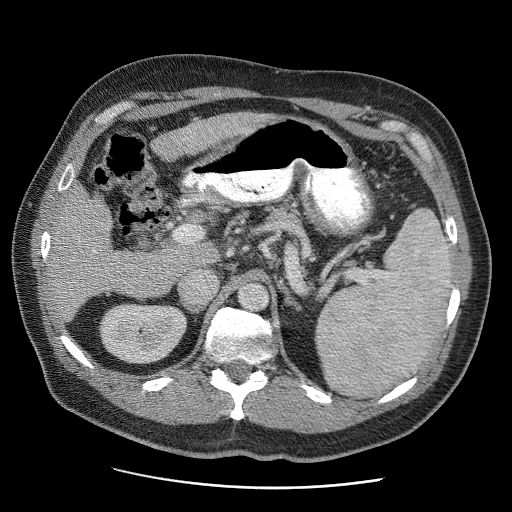
Contrast-enhanced abdominal CT (liver protocol), one axial slice; slice 23 of 81 in the series (ordered by position); reconstruction kernel STANDARD; soft-tissue window (W 400 / L 40 HU); 2.5 mm slice thickness; 512 × 512 image matrix, field of view 380 × 380 mm. Case-level facts recorded for this patient, not image findings: diagnosis: hepatocellular carcinoma (patient treated with transarterial chemoembolisation; whether this scan precedes or follows treatment is not stated here); TNM stage (as recorded): Stage-IIIA.
Annotated regions visible in this slice (semi-automatic segmentation, software-assisted and operator-edited):
- abdominal aorta: bounding box [x1, y1, x2, y2] px = [240, 284, 268, 311]
- liver parenchyma outside the tumour (the mass and vessels are separate outlines, so this box may not span the whole liver): [50, 112, 276, 319]